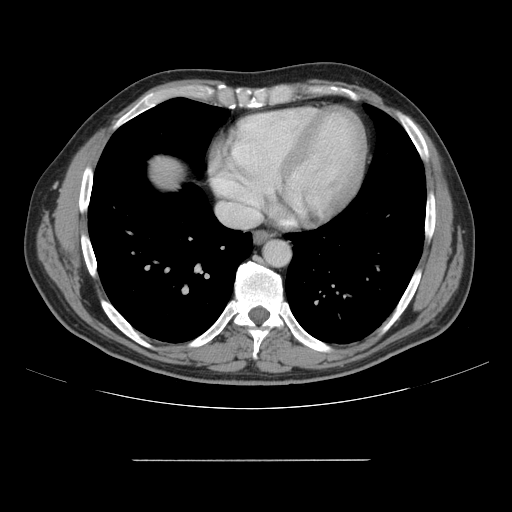
Contrast-enhanced abdominal CT, one axial slice. Position 152 of 164 along the scan axis. Intravenous contrast given. Soft-tissue window (W 400 / L 40 HU). 2.5 mm slice thickness. 512 × 512 image matrix, field of view 404 × 404 mm. Male patient, age 54 years. From the clinical record (not read from this slice): diagnosis: colorectal cancer liver metastases, imaged before liver resection; multiple liver metastases: yes; largest metastasis: 1 cm; disease in both lobes: no.
Outlined on this slice (expert manual segmentation):
- hepatic veins: box from (x=218, y=203) to (x=258, y=220) px
- liver: (x=151, y=159)–(x=180, y=185)
- planned liver remnant (the part of the liver to remain after resection): (x=152, y=159)–(x=181, y=186)